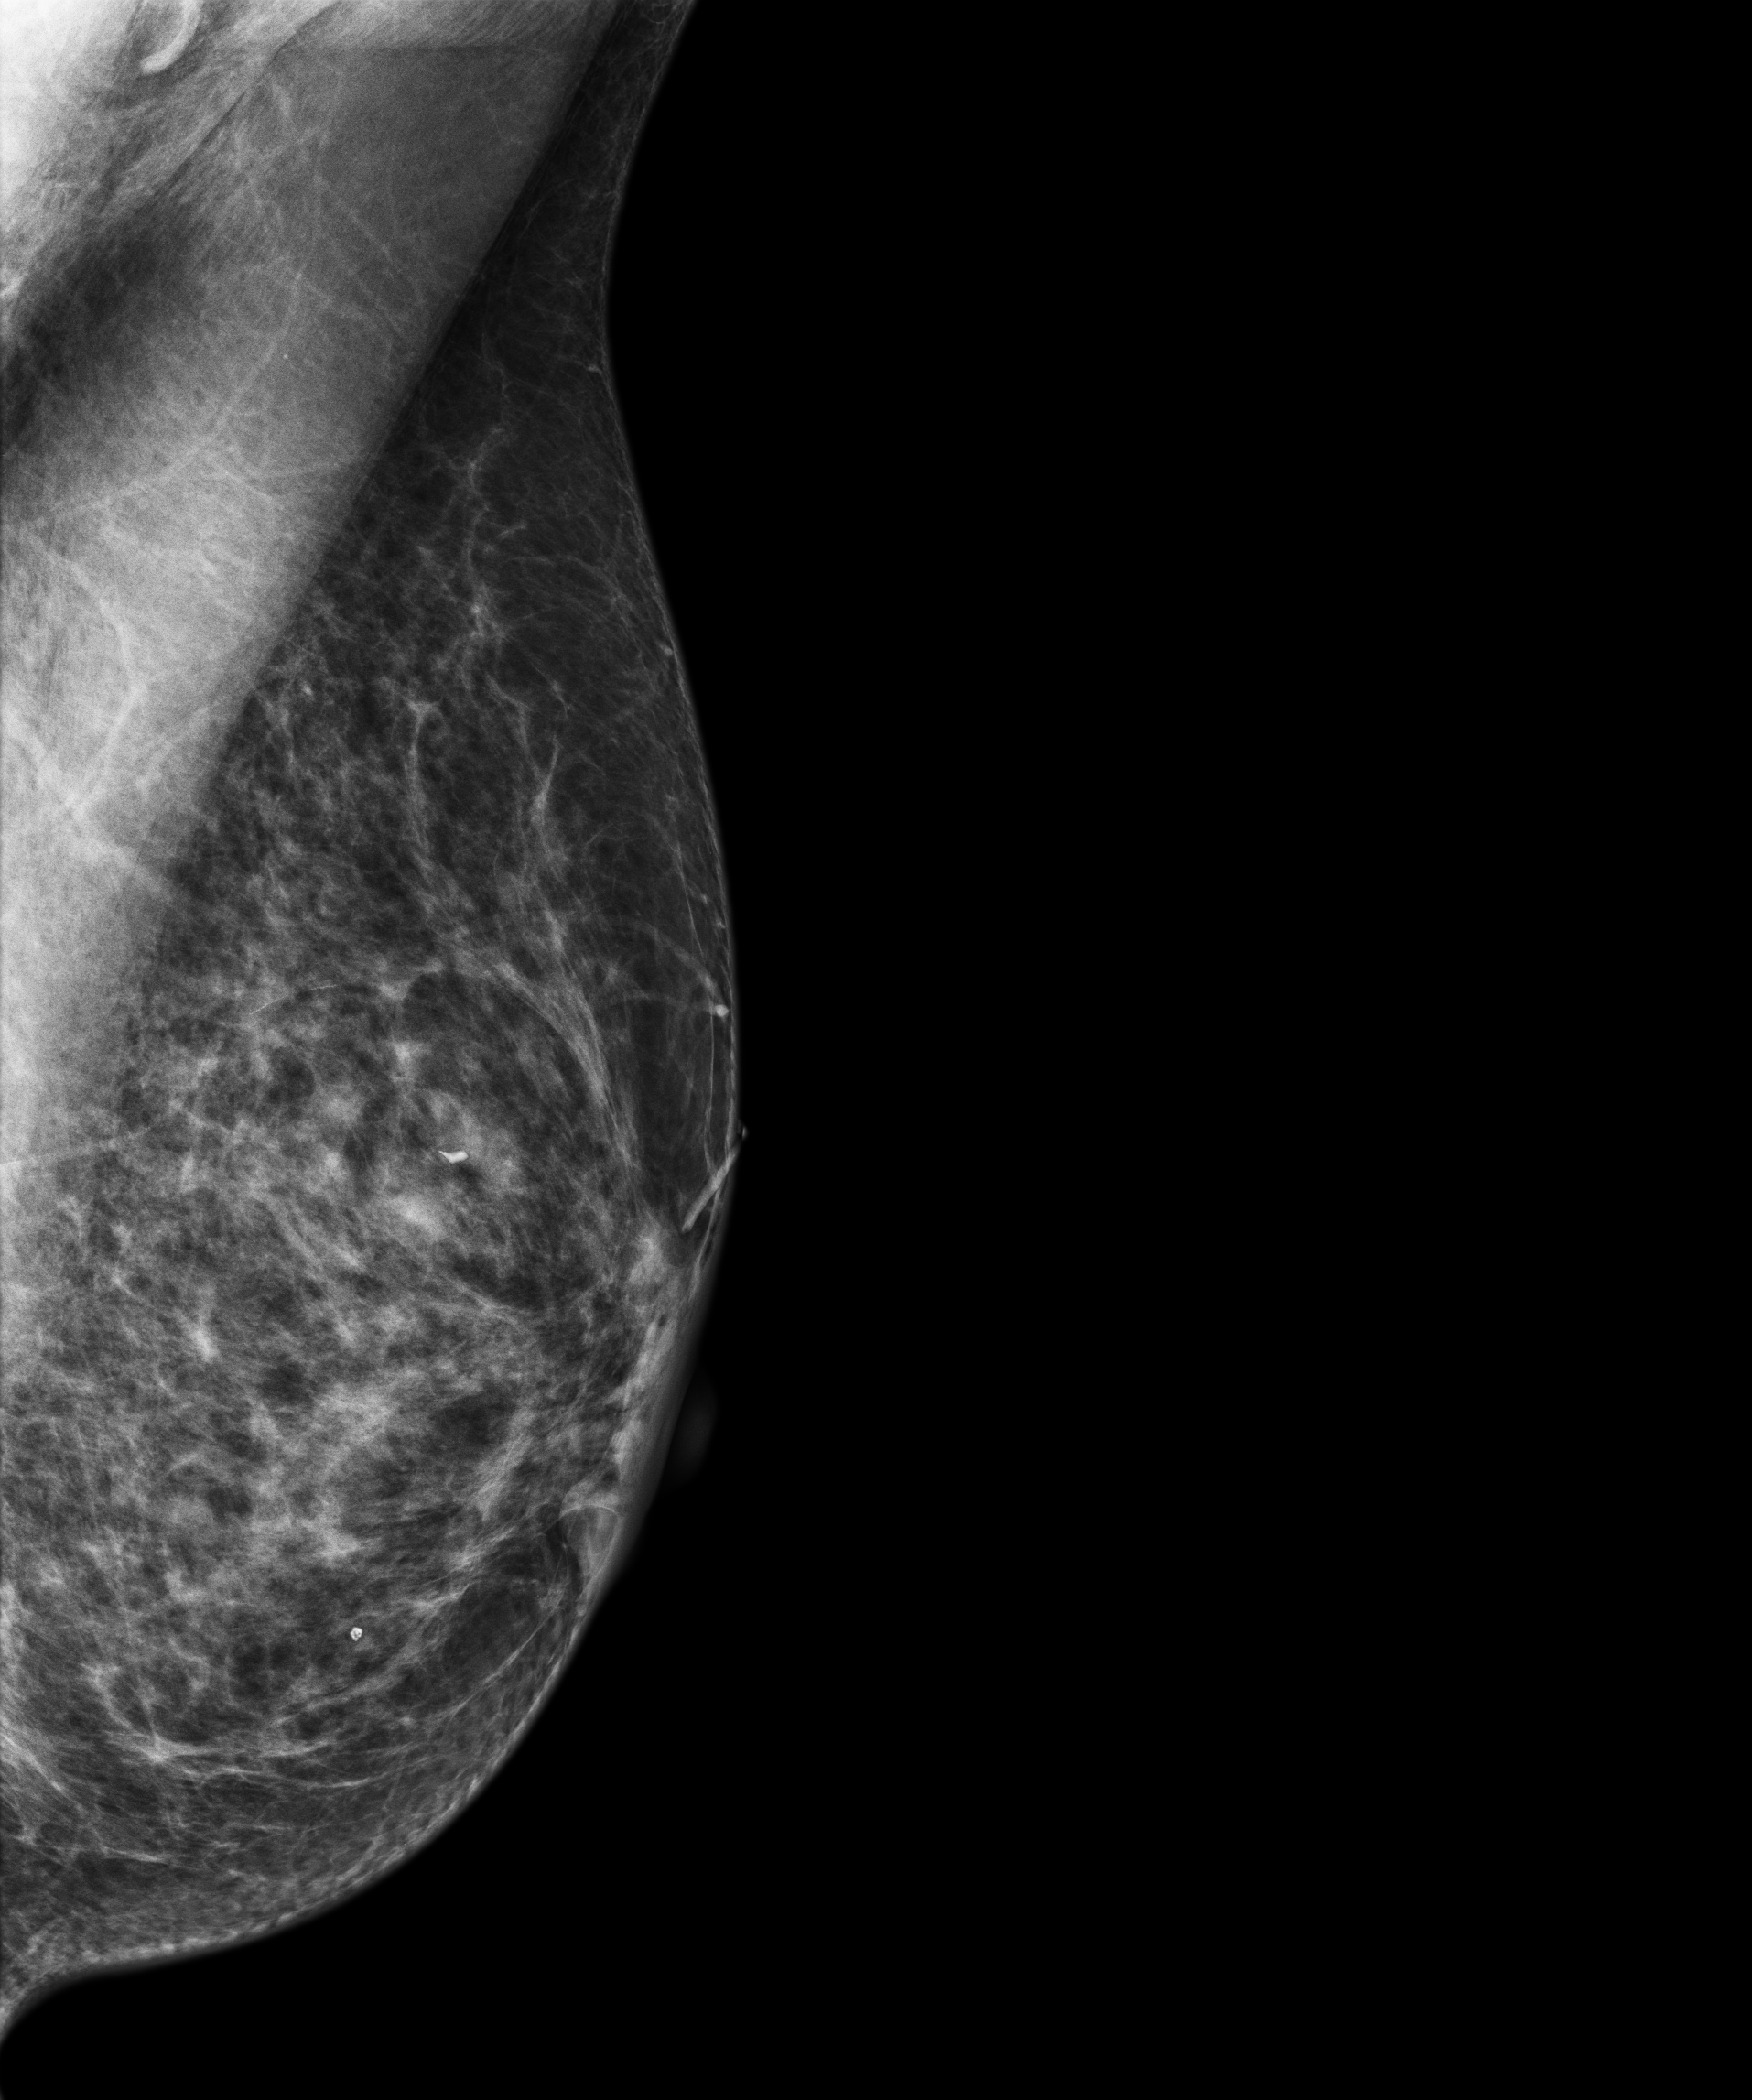
Annual screening mammography examination; compressed breast thickness 55 mm. Patient aged 70 years (female).
Image type: full-field digital mammogram. Breast: left. Projection: mediolateral oblique (MLO) view.